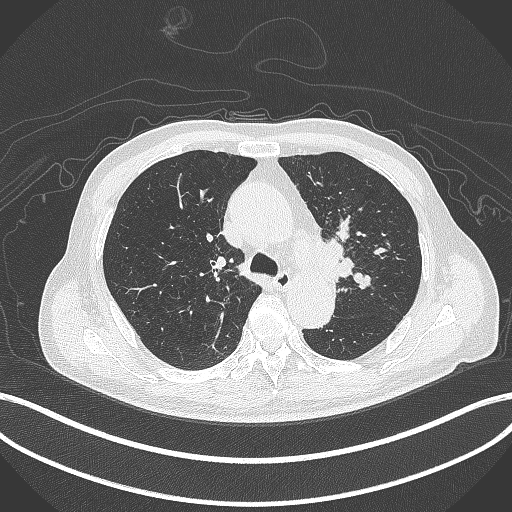
Chest CT, one axial slice; lung window (W 1500 / L -600 HU); 1 mm slice thickness; 512 × 512 image matrix, field of view 400 × 400 mm. Patient: male, 77 years. Case-level facts recorded for this patient, not image findings: clinical TNM (as recorded): T3 N1 M0.
Structures marked on this image (rectangle marked by the reading radiologist):
- lung tumour (recorded histology: adenocarcinoma): box from (x=314, y=235) to (x=361, y=287) px